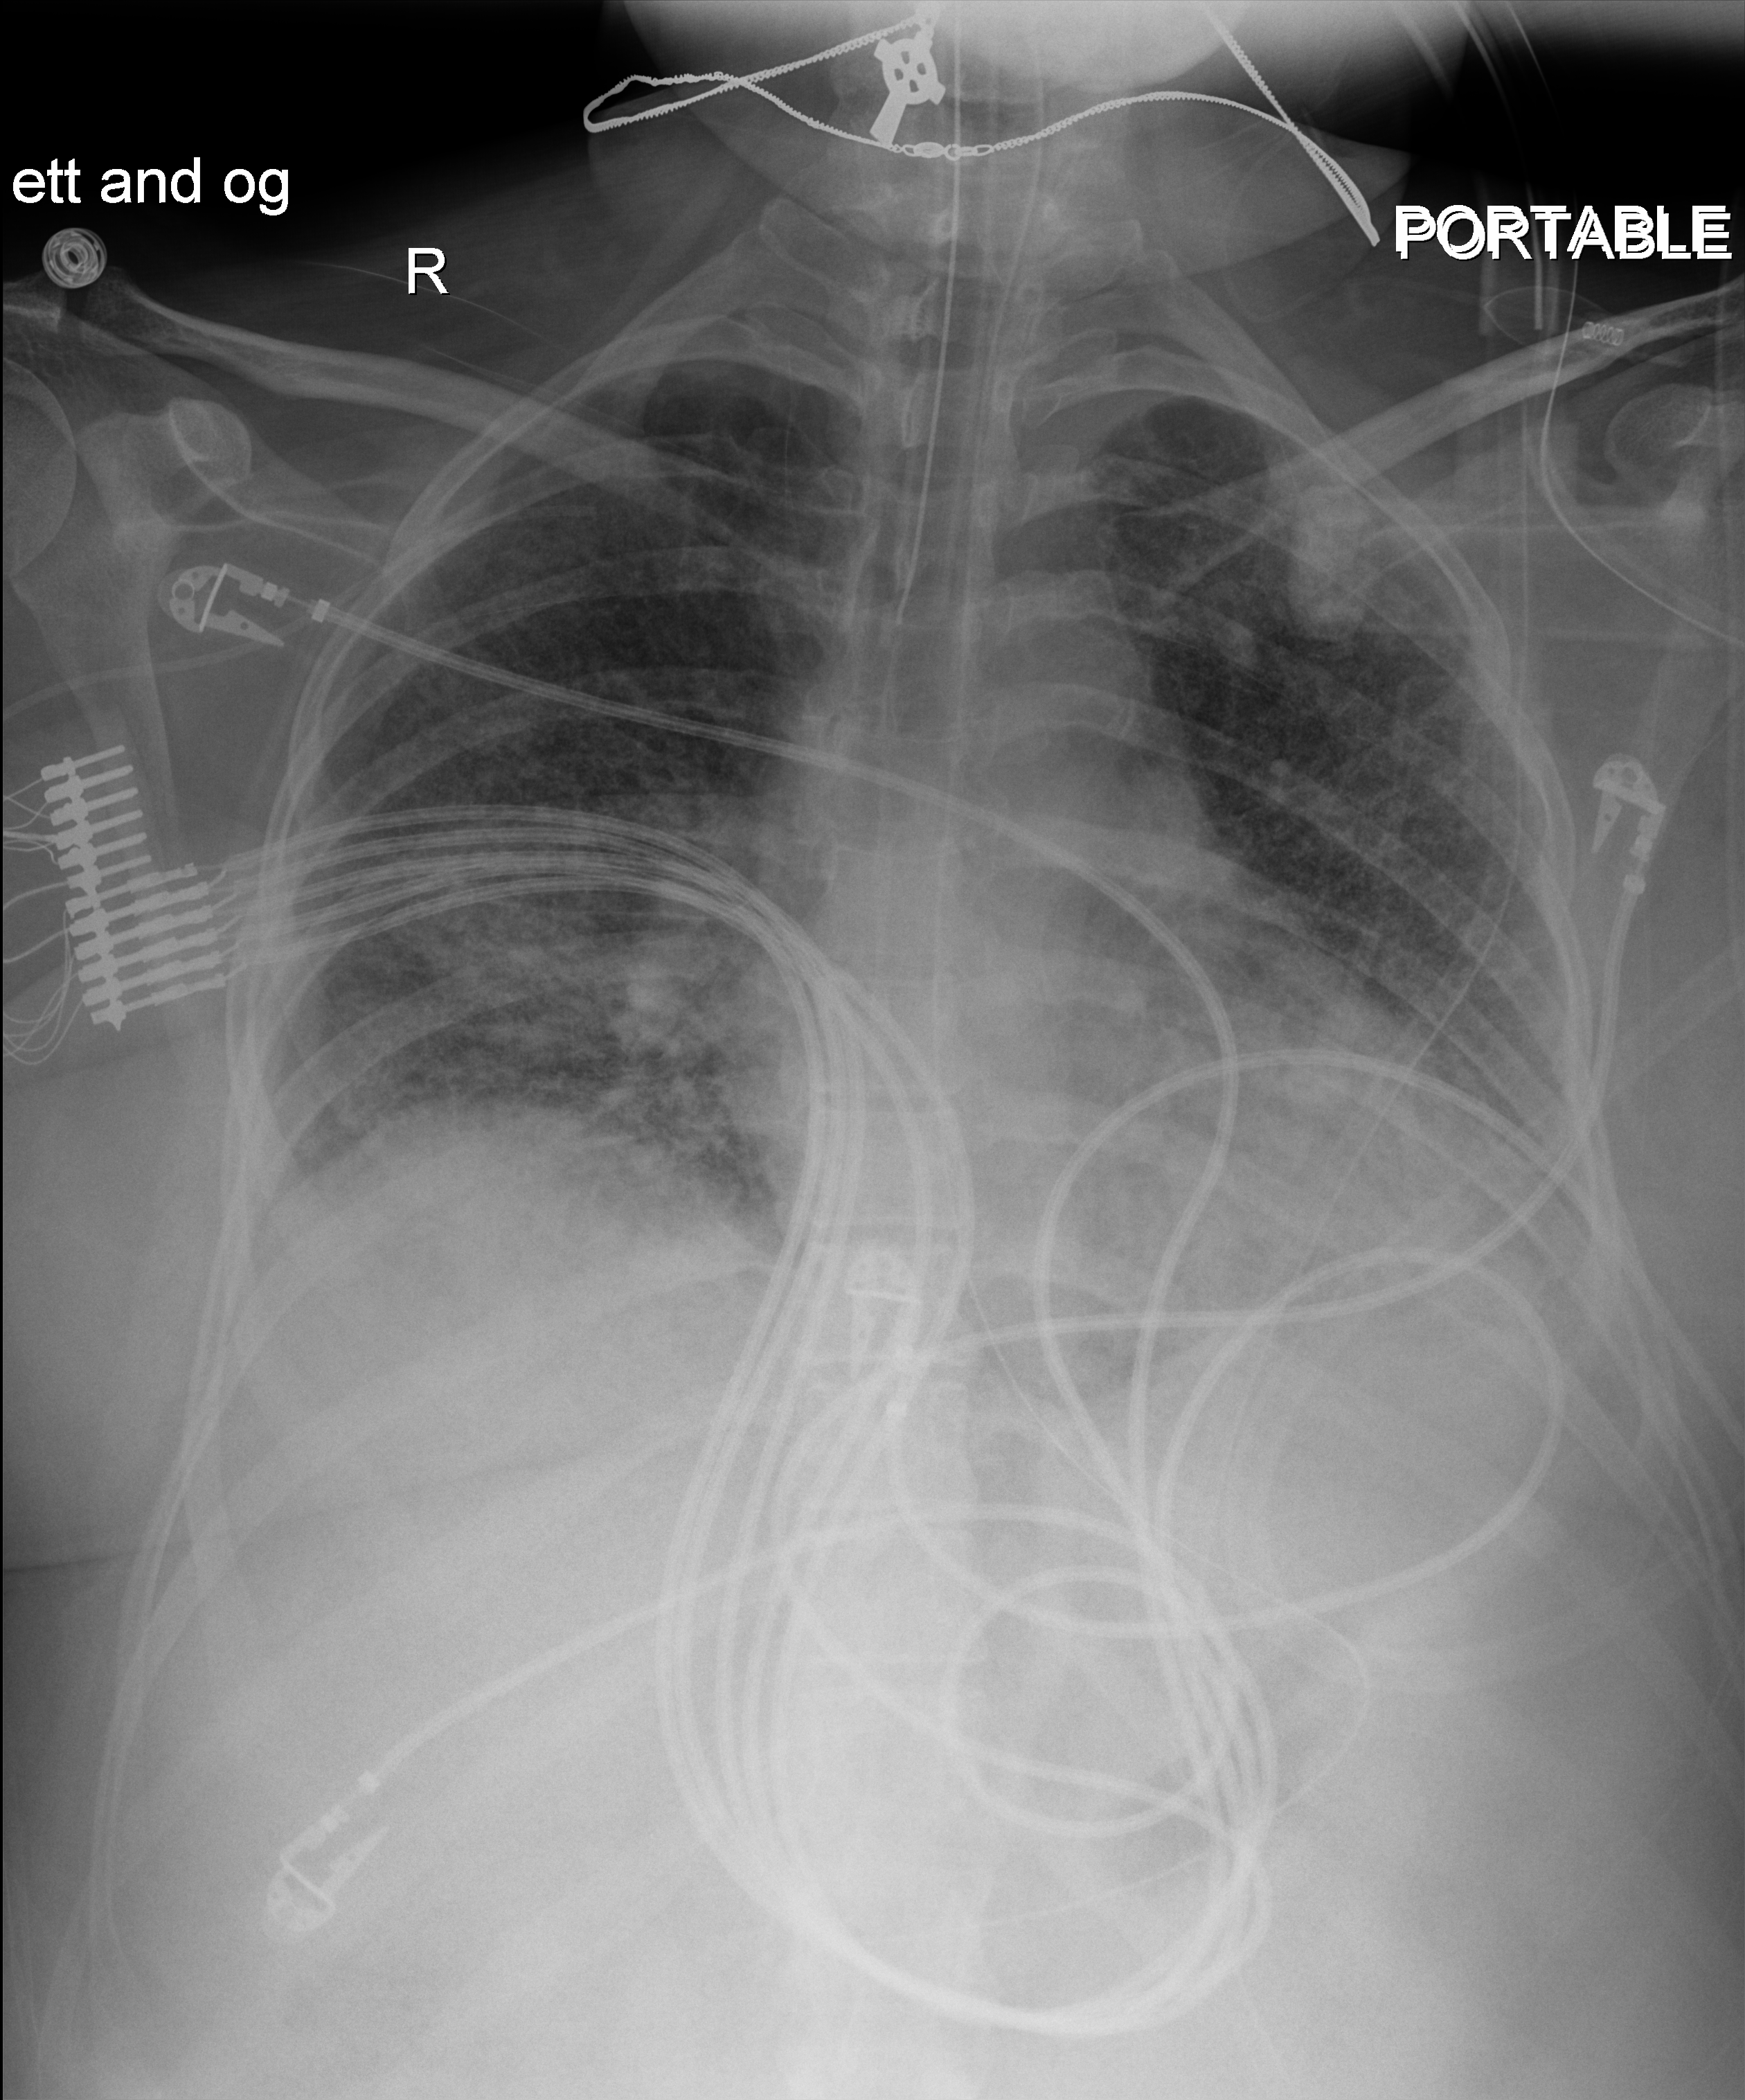
Portable chest radiograph; anteroposterior (AP) projection. Female patient hospitalised with COVID-19, age 18–59 years.
From the hospital-stay record, not from the radiograph (when in the stay this image was taken is not recorded): chronic kidney disease (admission record): no; hypertension (admission record): no.